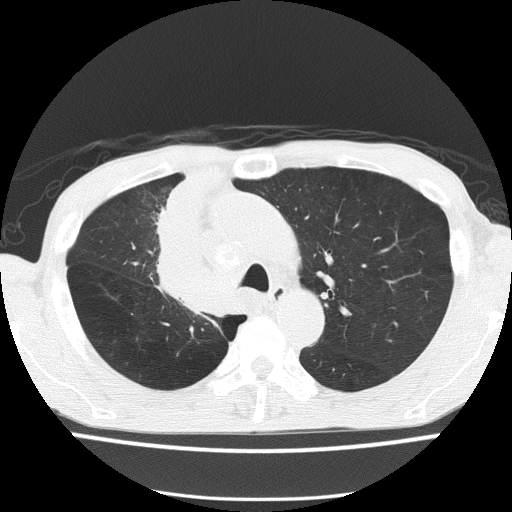
Low-dose screening chest CT, one axial slice. Position 105 of 150 along the scan axis. Lung window (W 1500 / L -600 HU). 512 × 512 image matrix, field of view 336 × 336 mm.
Annotated regions visible in this slice (expert manual segmentation):
- lesion 1 (tumor, hilum of right lung): bounding box (x1, y1, x2, y2) in pixels: (159, 180, 226, 312)